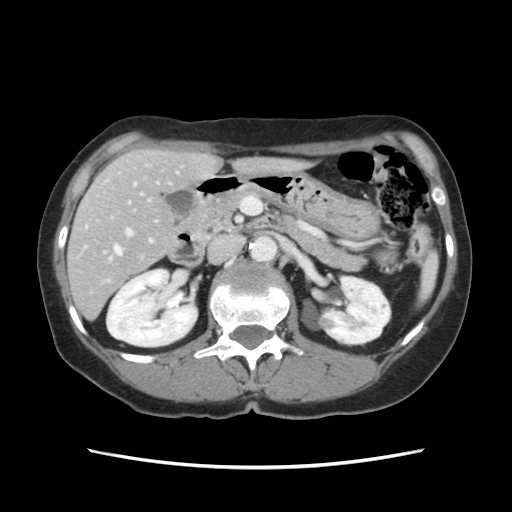
Contrast-enhanced abdominal CT, one axial slice. Slice 59 of 120 in the series (ordered by position). 120 kVp. Soft-tissue window (W 400 / L 40 HU). 512 × 512 image matrix. Female patient, age 70 years. Case-level facts recorded for this patient, not image findings: diagnosis: colorectal cancer liver metastases, imaged before liver resection; multiple liver metastases: no; largest metastasis: 2.5 cm; chemotherapy before resection: yes.
Annotated regions visible in this slice (outlined manually by an expert reader):
- hepatic veins: bounding box [x1, y1, x2, y2] px = [114, 246, 121, 255]
- liver: [69, 150, 293, 317]
- planned liver remnant (the part of the liver to remain after resection): [70, 150, 293, 292]
- portal vein (with intrahepatic branches): [126, 172, 178, 243]